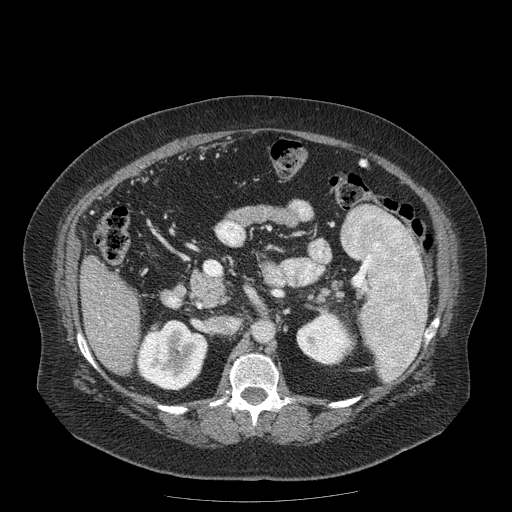
Contrast-enhanced abdominal CT (liver protocol), one axial slice. Slice 71 of 204 in the series (ordered by position). 120 kVp. Soft-tissue window (W 400 / L 40 HU). 2.5 mm slice thickness. 512 × 512 image matrix, field of view 440 × 440 mm. Case-level facts recorded for this patient, not image findings: diagnosis: hepatocellular carcinoma (patient treated with transarterial chemoembolisation; whether this scan precedes or follows treatment is not stated here); TNM stage (as recorded): Stage-IIIB; Child-Pugh class: A; tumour differentiation: well differentiated.
Outlined on this slice (semi-automatically segmented with operator editing):
- liver parenchyma outside the tumour (the mass and vessels are separate outlines, so this box may not span the whole liver): bounding box (x1, y1, x2, y2) in pixels: (80, 256, 140, 374)